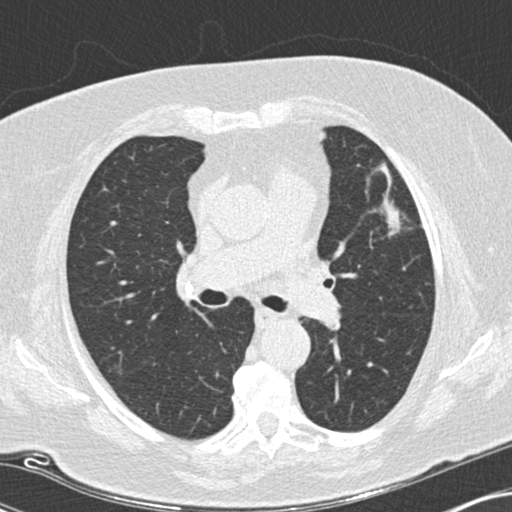
Low-dose screening chest CT, one axial slice; slice 97 of 151 in the series (ordered by position); lung window (W 1500 / L -600 HU); 2 mm slice thickness; 512 × 512 image matrix, field of view 330 × 330 mm.
Outlined on this slice (outlined manually by an expert reader):
- lesion 1 (tumor, upper lobe of left lung): bounding box <380,202,401,237> (left, top, right, bottom; pixels)